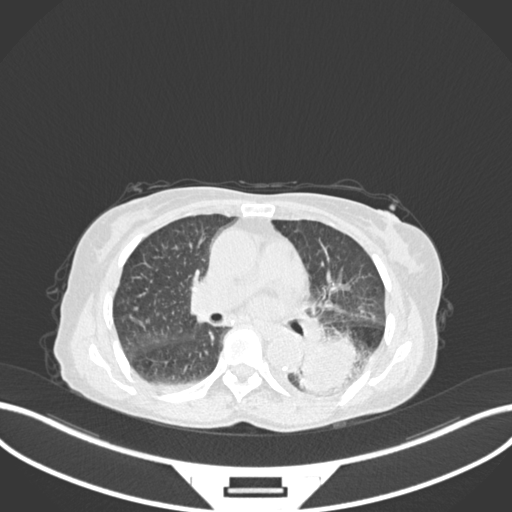
Chest CT, one axial slice. Slice 94 of 233 in the series (ordered by position). 120 kVp. Lung window (W 1500 / L -600 HU). 512 × 512 image matrix, field of view 400 × 400 mm. Female patient, age 78 years. Case-level facts recorded for this patient, not image findings: clinical TNM (as recorded): T3 N0 M1.
Outlined on this slice (bounding box drawn by a radiologist):
- lung tumour (recorded histology: squamous cell carcinoma): bounding box (x1, y1, x2, y2) in pixels: (295, 333, 364, 398)